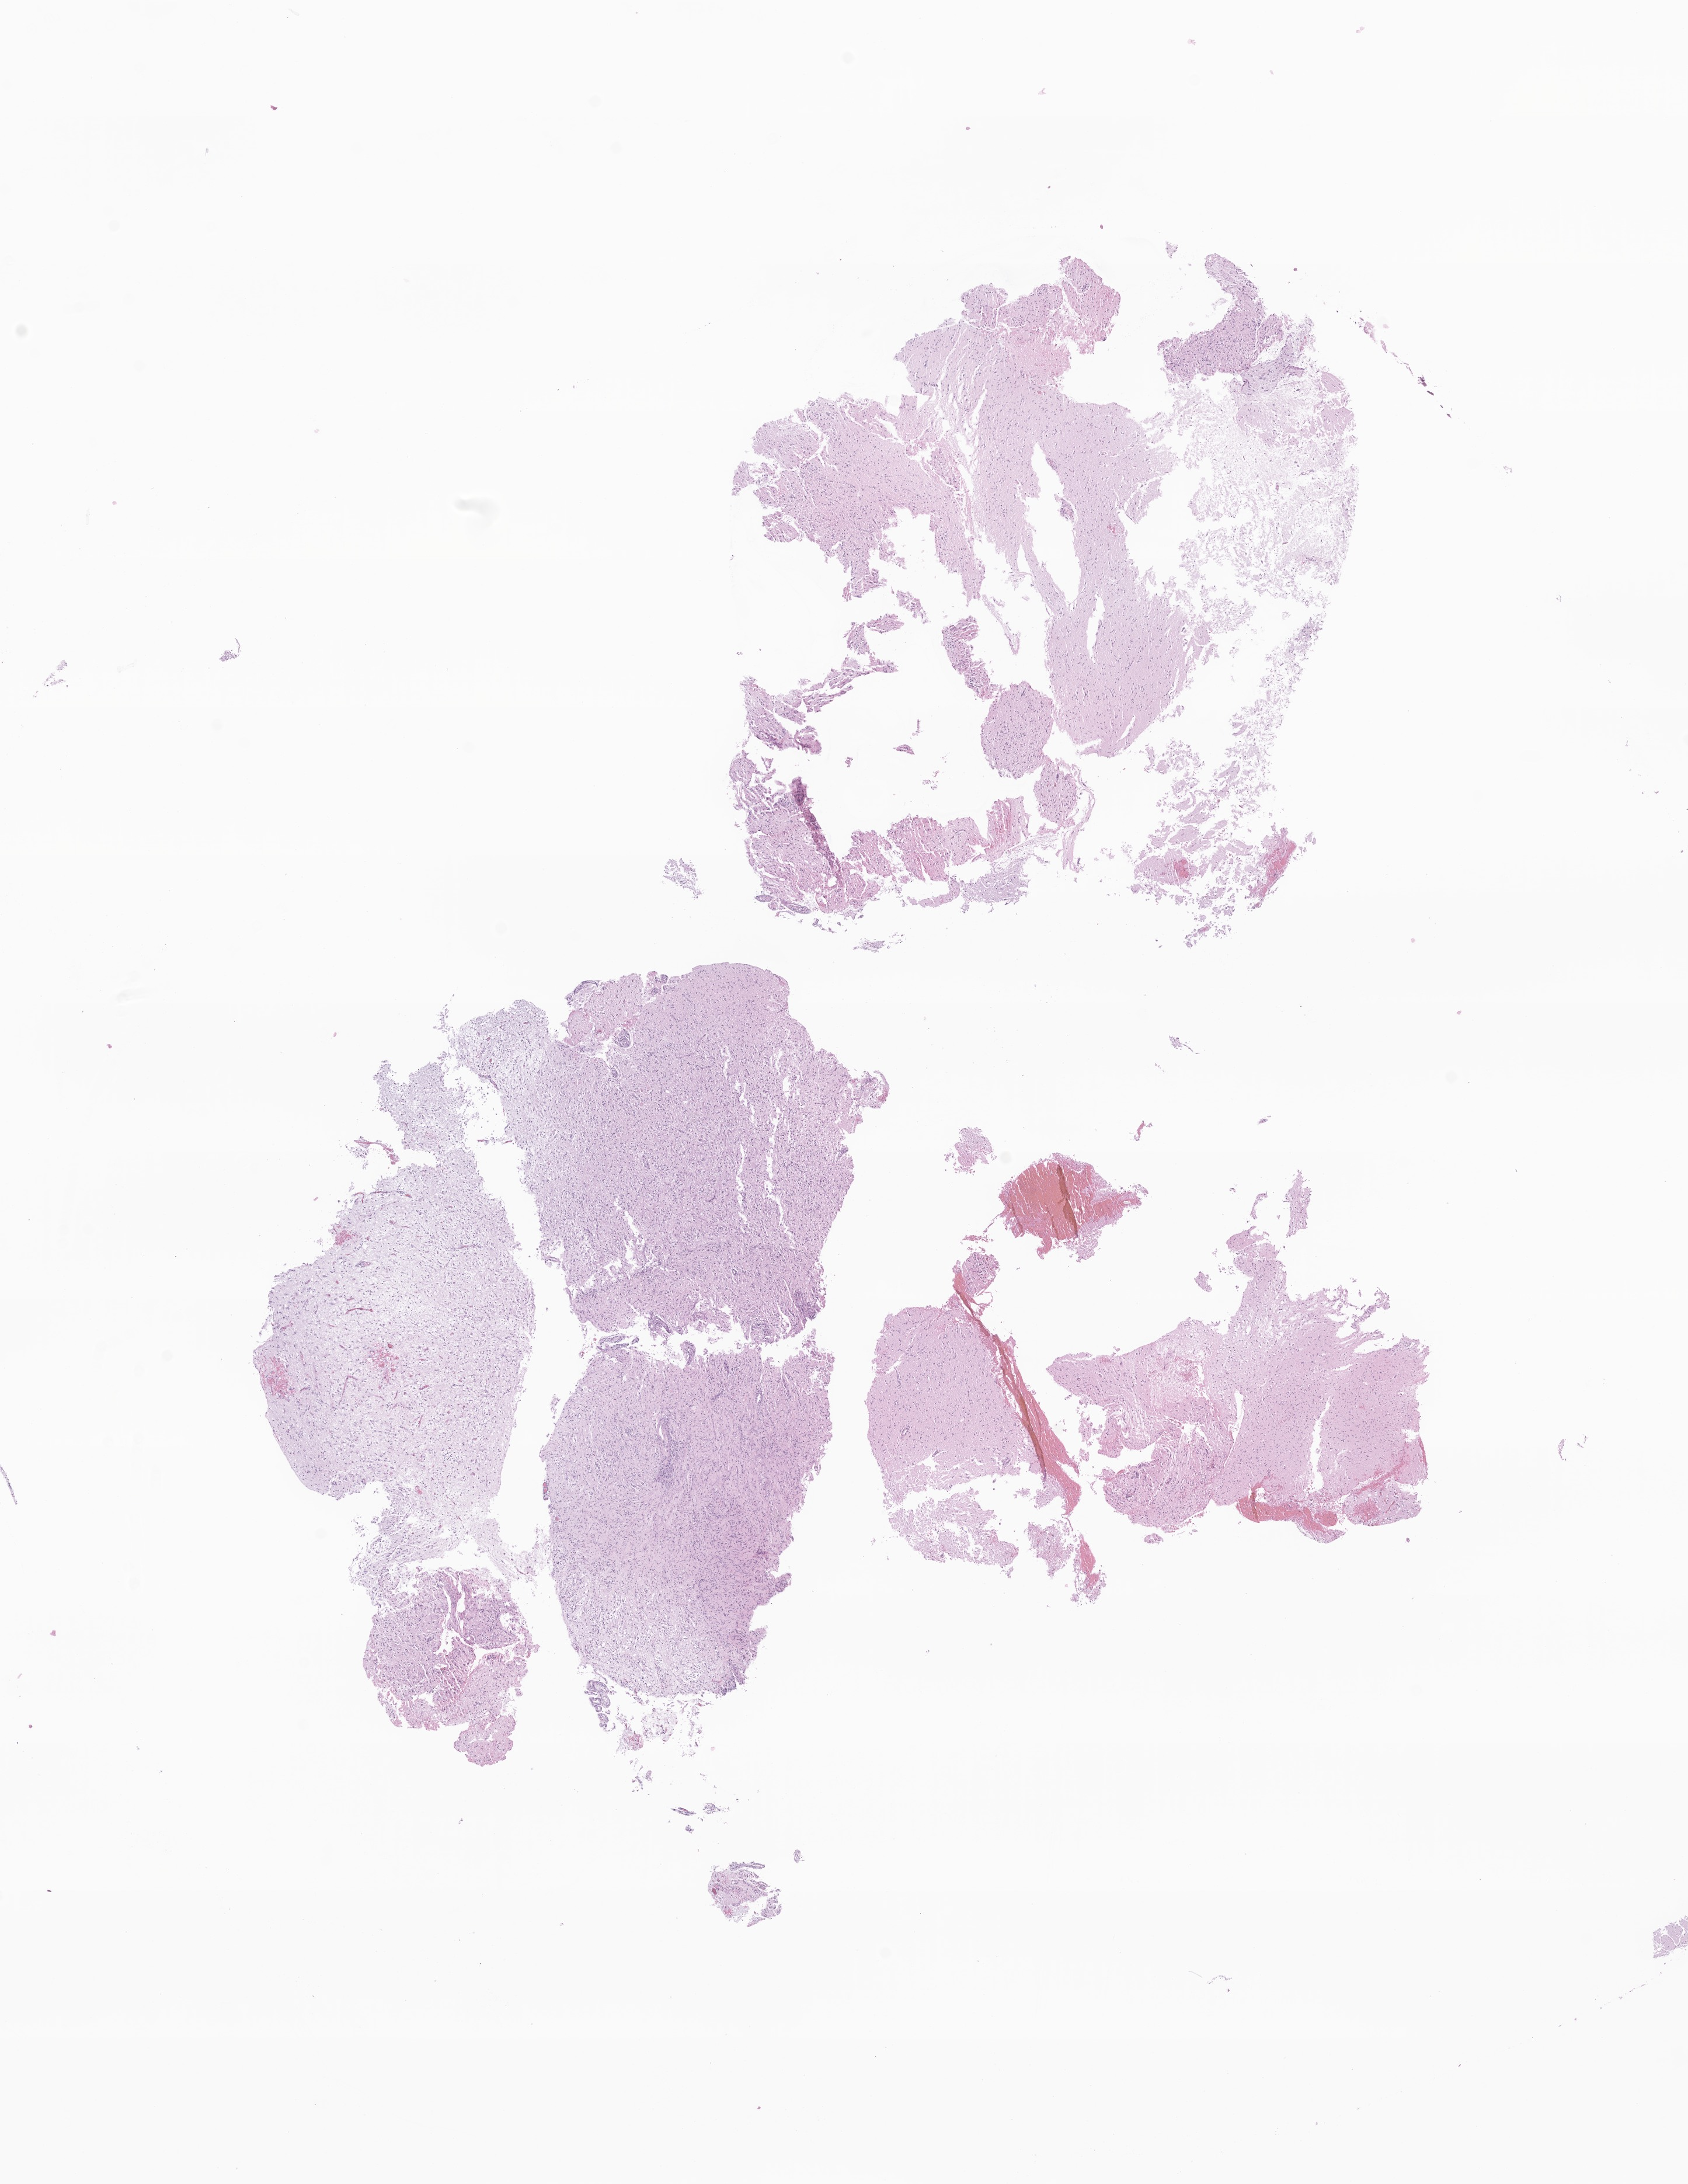
Whole-slide image, H&E stain of tumor tissue from the brain, whole scanned area (about 12.2 x 15.8 mm) shown as a low-resolution overview; FFPE section. Patient male; age 135 months (11 years 3 months).
Diagnosis (ICD-O-3 morphology term): Tumor cells, uncertain whether benign or malignant.